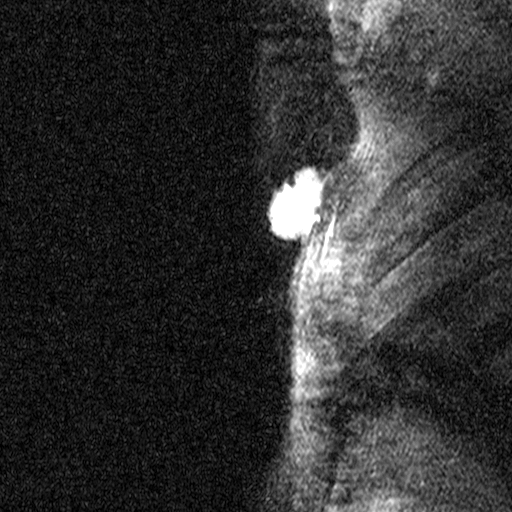
Breast MRI (dynamic contrast-enhanced), one sagittal slice; slice 38 of 44 in the series (ordered by position); dynamic contrast-enhanced study with each time point stored as its own series, time point 2 of 3 at this slice position (early post-contrast, ordered by acquisition time); 1.5 T; TE 4.5 ms, TR 11 ms; 3 mm slice thickness; 512 × 512 image matrix. Patient: female, 44 years. Case-level facts recorded for this patient, not image findings: setting: breast cancer imaged before/during neoadjuvant chemotherapy; receptor status: HR-positive, HER2-negative.
Annotated regions visible in this slice (semi-automatic segmentation, software-assisted and operator-edited):
- analysis volume of interest (the breast-tissue region the enhancement analysis was run in; not a lesion): bounding box <218,118,341,291> (left, top, right, bottom; pixels)
- tumour enhancement mask (voxels above the 90 % enhancement threshold inside the analysis volume of interest): <268,167,323,239>